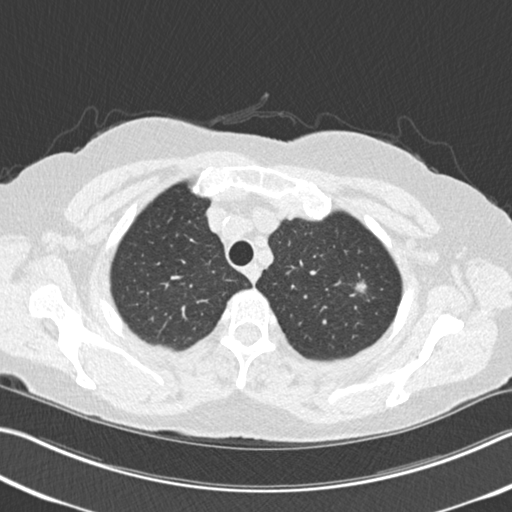
Axial slice from a low-dose chest CT screening exam, second annual screen, lung window (W 1500 / L -600 HU), 2 mm slice thickness, 120 kVp. Female, age 64 years at enrolment.
- Expert-annotated lung lesion, bounding box [x1, y1, x2, y2] px = [346, 270, 380, 303].
- The exam's reader record, not a measurement of the box and not confirmed to be the same lesion: non-calcified nodule or mass ≥4 mm, left upper lobe, 13 × 10 mm, spiculated (stellate) margins, soft tissue attenuation, pre-existing on the prior screen: yes; interval growth: yes.
- Official screen result: positive, other.
- Participant outcome: lung cancer diagnosed 106 days after this screen — signet ring cell carcinoma, right upper lobe, poorly differentiated (G3), stage IA (AJCC 6th edition), 15 mm at pathology.